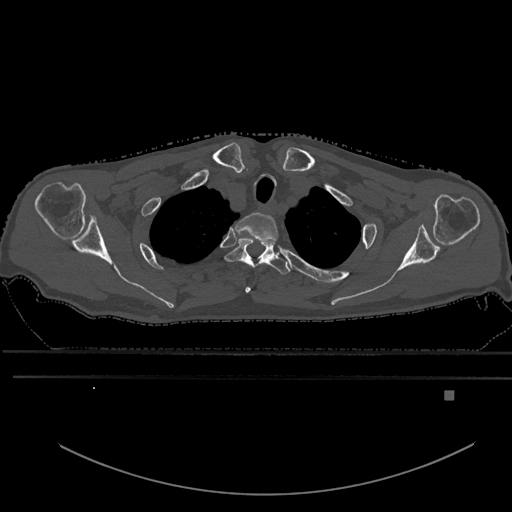
CT including the spine, one axial slice; slice 507 of 969 in the series (ordered by position); bone window (W 1800 / L 400 HU); 512 × 512 image matrix, field of view 456 × 456 mm. Patient: male, 82 years. From the clinical record (not read from this slice): primary cancer: prostate; vertebrae with lytic lesions (as recorded): T11, T9, T8, T2.
Outlined on this slice (semi-automatic segmentation, software-assisted and operator-edited):
- T1 vertebra: bounding box [x1, y1, x2, y2] px = [235, 212, 279, 293]
- T2 vertebra: [225, 238, 291, 275]